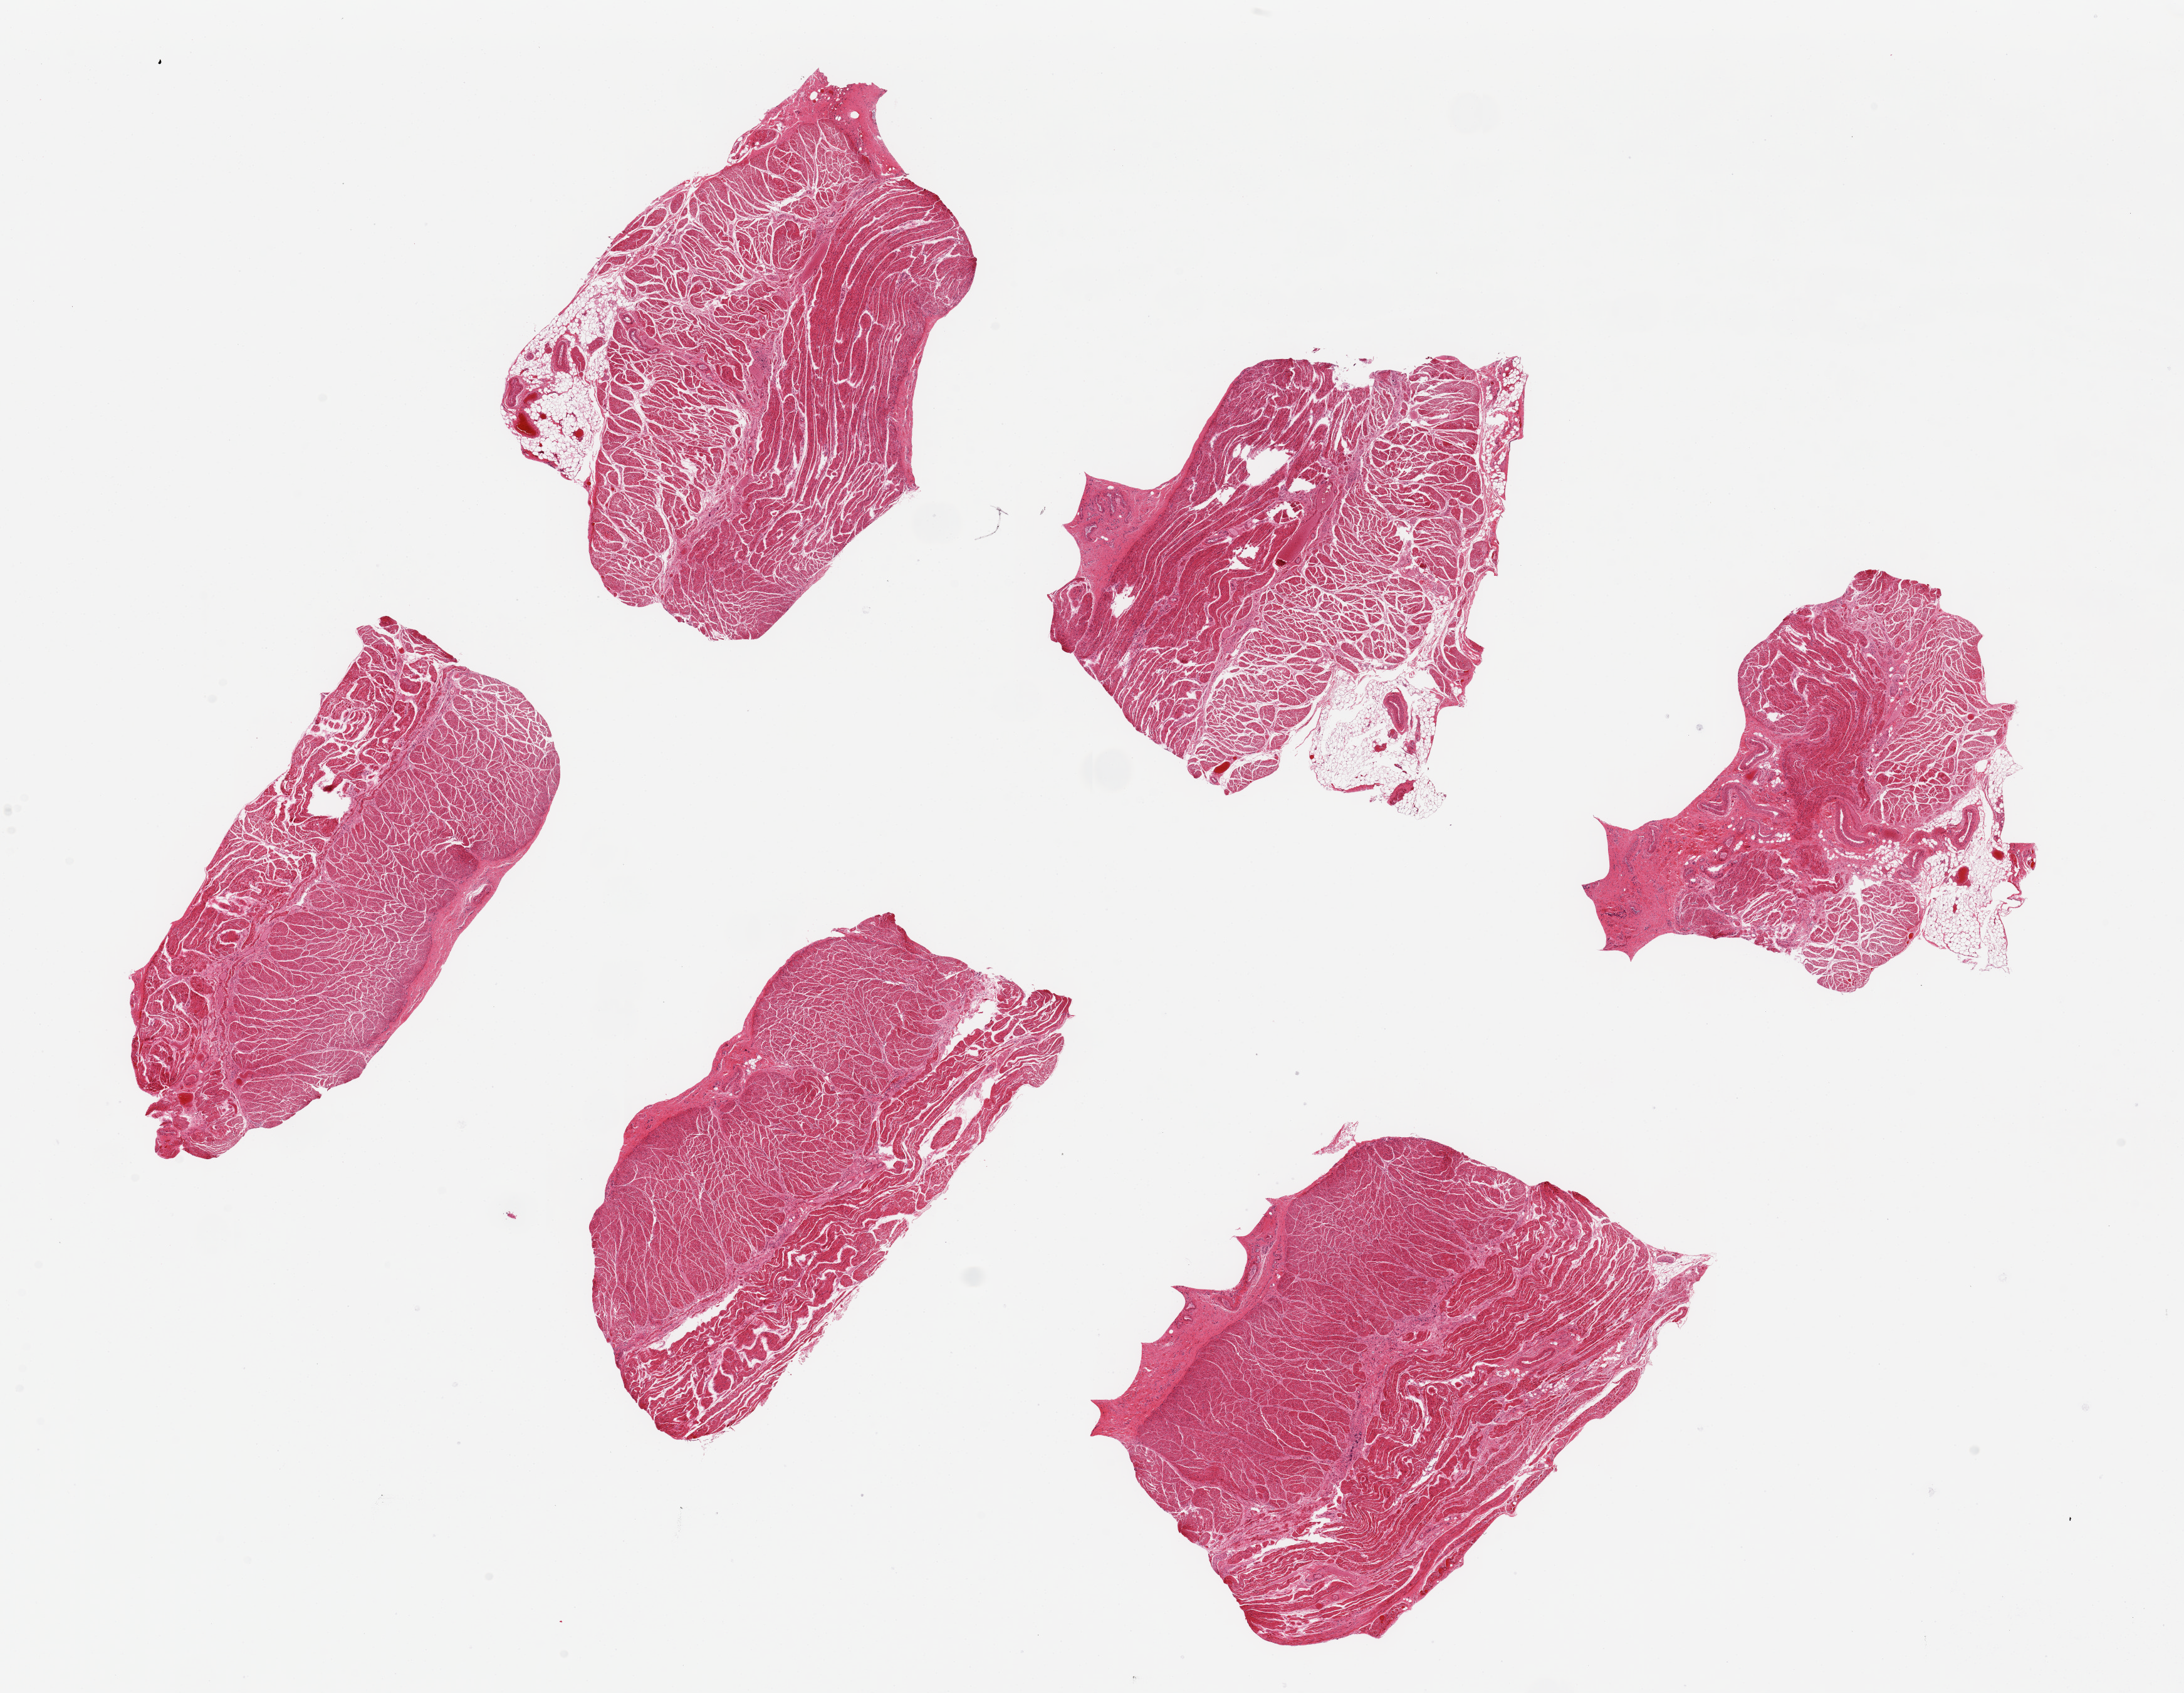
Digitized H&E-stained section — whole scanned area (about 27.6 x 21.4 mm, acquisition: 20x scan) shown as a low-resolution overview, PAXgene-fixed, paraffin-embedded tissue, section of esophageal muscle (target tissue), tissue donor sample. Donor sex: male.
Review note (as recorded): 6 pieces, ~6.8x4.6mm; largest have cassette markings.